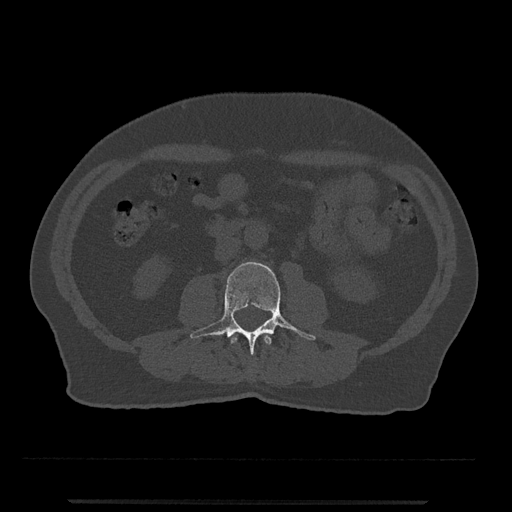
CT including the spine, one axial slice. Position 205 of 797 along the scan axis. 120 kVp. Bone window (W 1800 / L 400 HU). 0.5 mm slice thickness. 512 × 512 image matrix. Patient: male, 63 years. From the clinical record (not read from this slice): primary cancer: prostate.
Outlined on this slice (semi-automatically segmented with operator editing):
- L2 vertebra: bounding box <230,333,272,345> (left, top, right, bottom; pixels)
- L3 vertebra: <190,262,316,355>